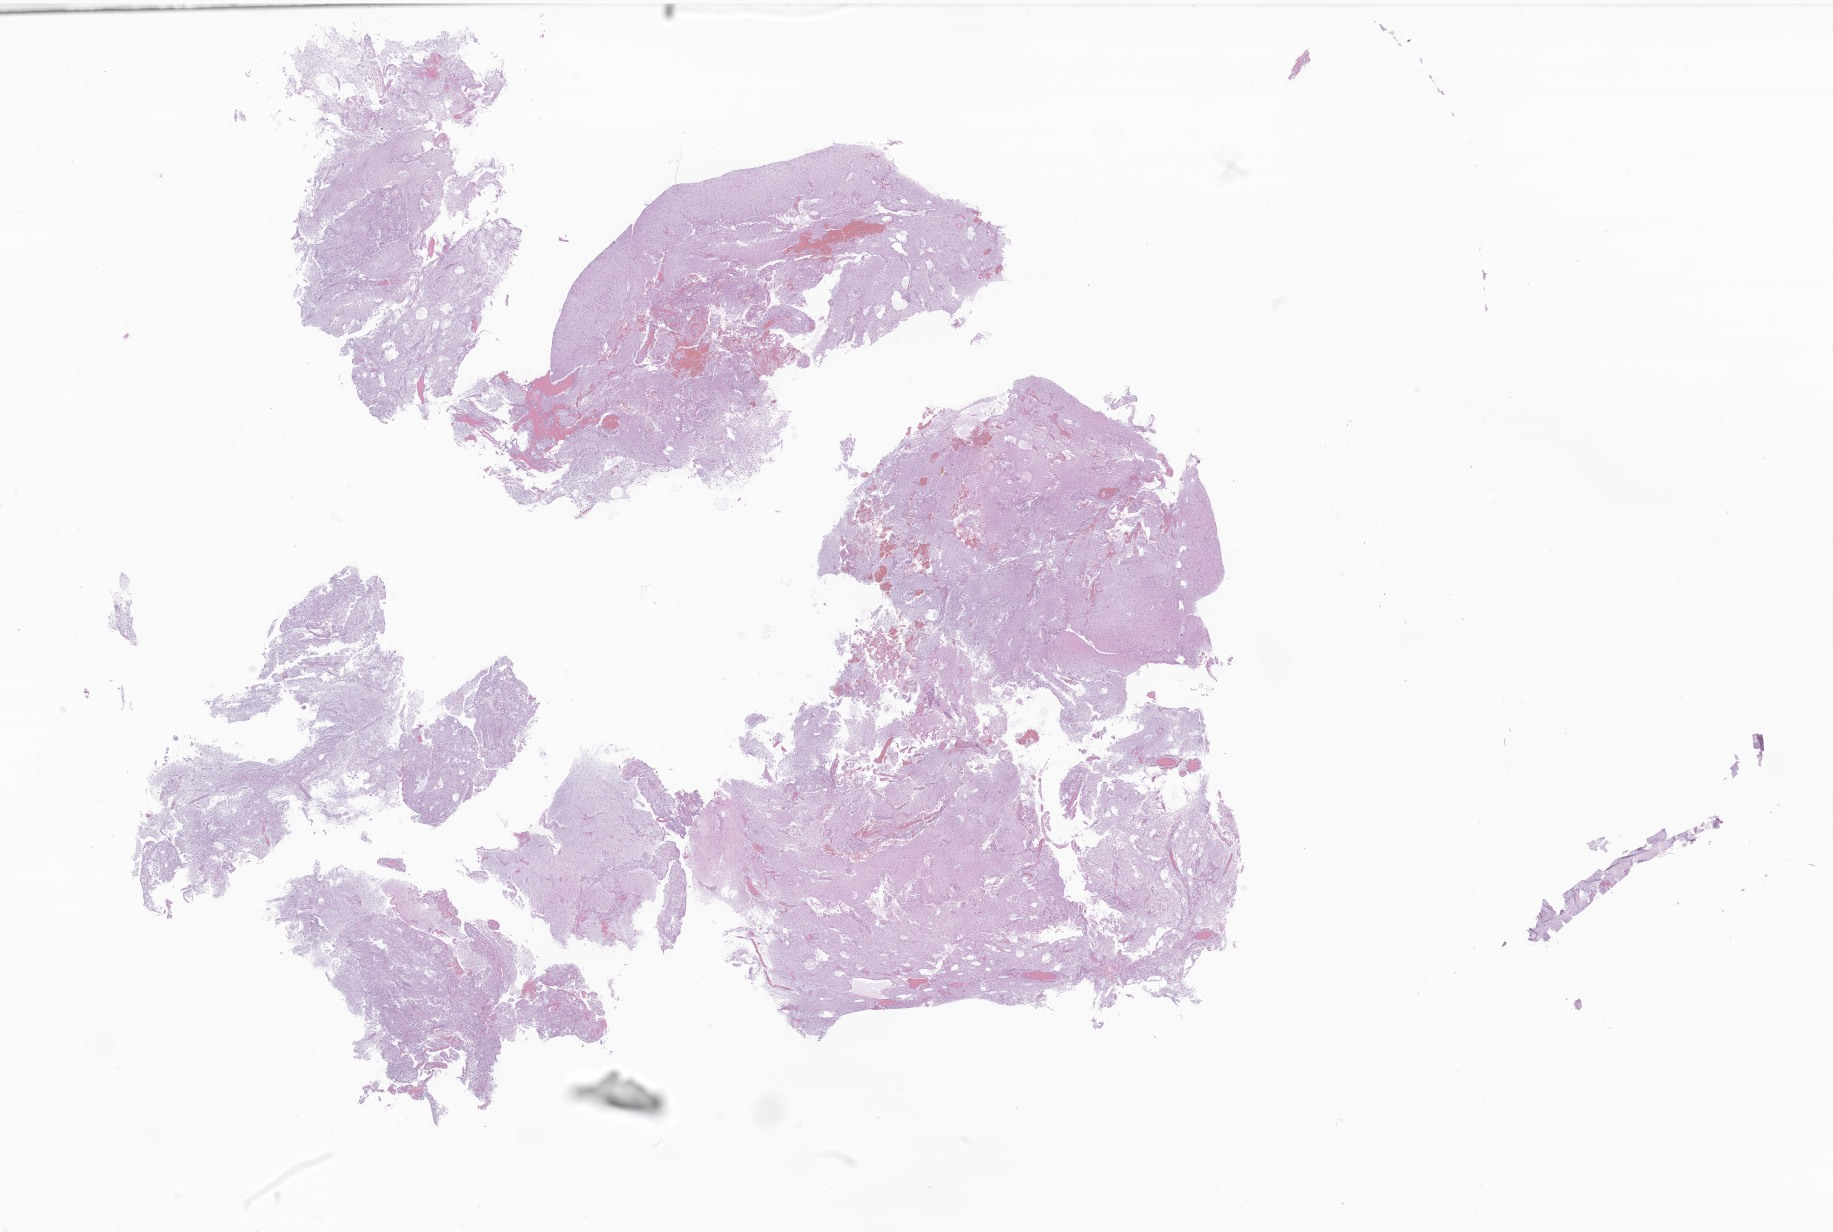
Digitized H&E-stained section of tumor tissue from the brain — a low-resolution overview of the entire scanned area, about 30.9 x 20.8 mm; formalin-fixed, paraffin-embedded (FFPE) tissue. Female patient, age 97 months (8 years 1 month).
Diagnosis: Pilocytic astrocytoma.